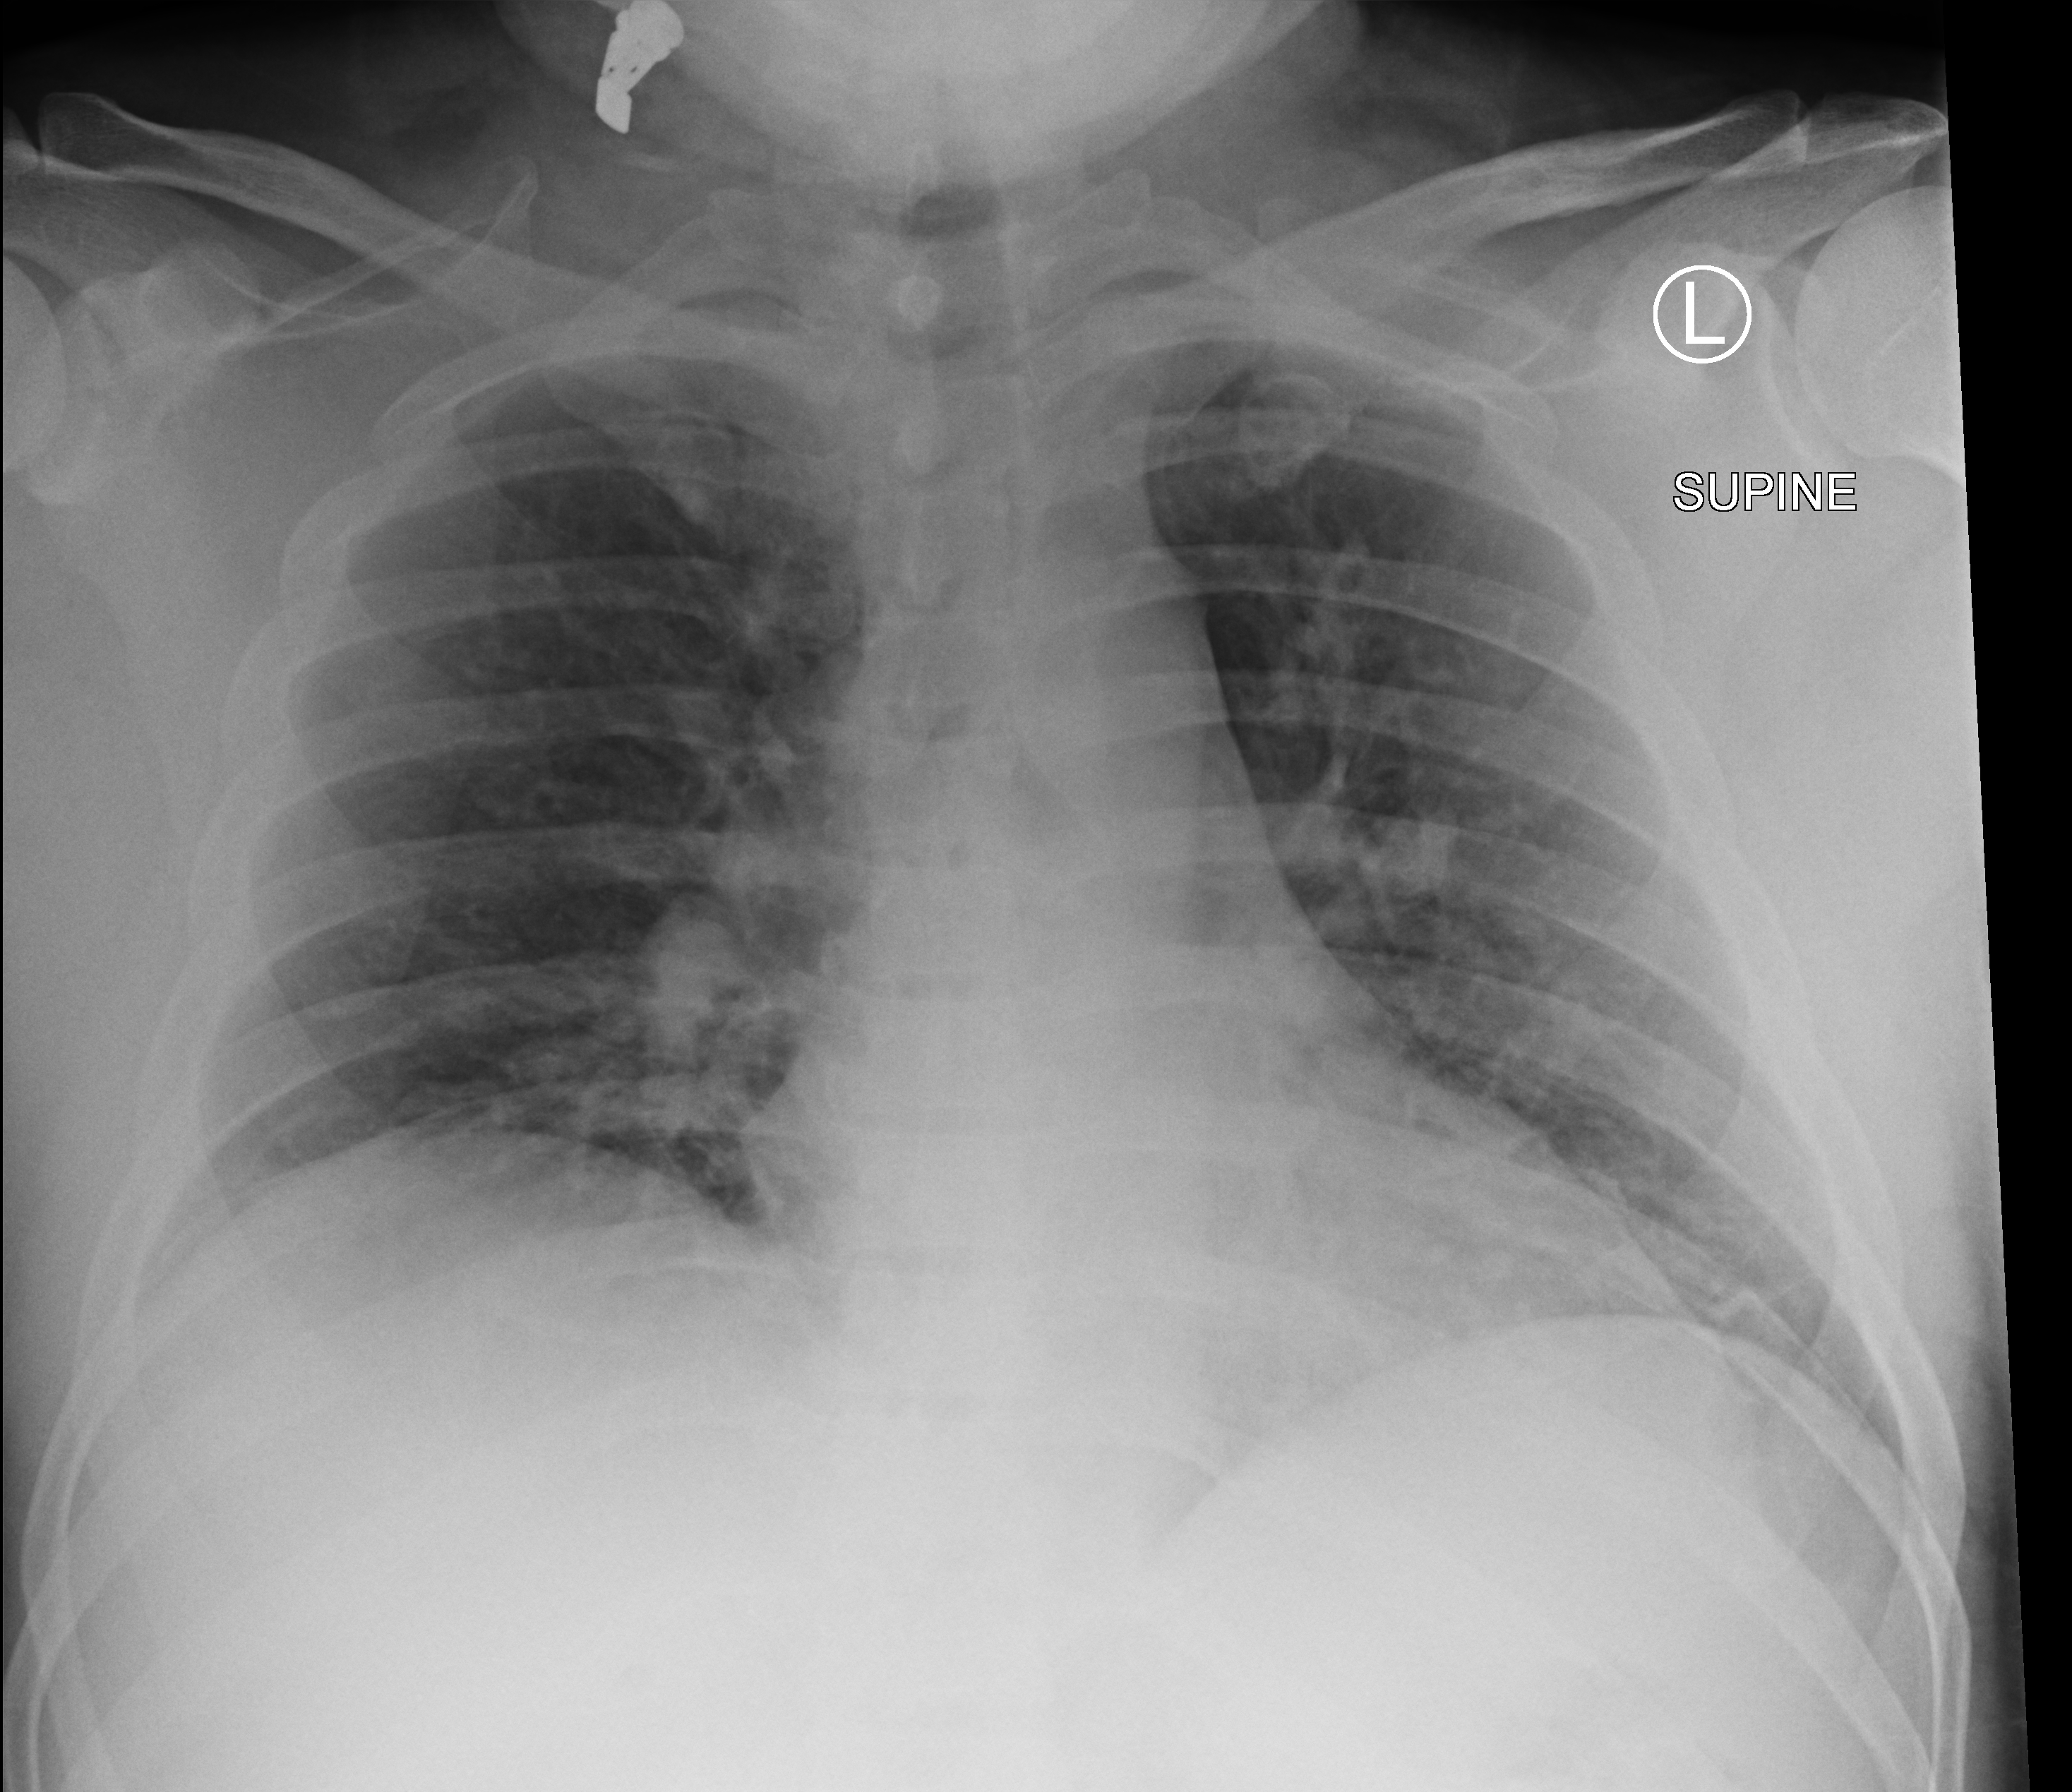
Chest X-ray (portable), anteroposterior (AP) projection. Male patient hospitalised with COVID-19, age 18–59 years.
From the hospital-stay record, not from the radiograph (when in the stay this image was taken is not recorded): mechanically ventilated during this hospital stay: no.